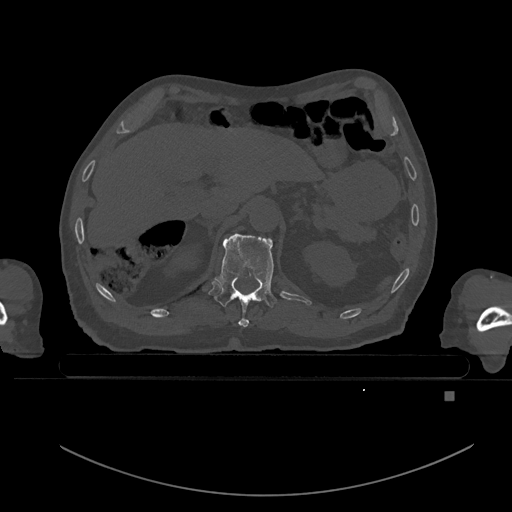
CT including the spine, one axial slice. Bone window (W 1800 / L 400 HU). 0.5 mm slice thickness. 512 × 512 image matrix, field of view 456 × 456 mm. Male patient, age 82 years. From the clinical record (not read from this slice): primary cancer: prostate; vertebrae with lytic lesions (as recorded): T11, T9, T8, T2.
Outlined on this slice (semi-automatic segmentation, software-assisted and operator-edited):
- T11 vertebra: bounding box (x1, y1, x2, y2) in pixels: (214, 233, 278, 327)